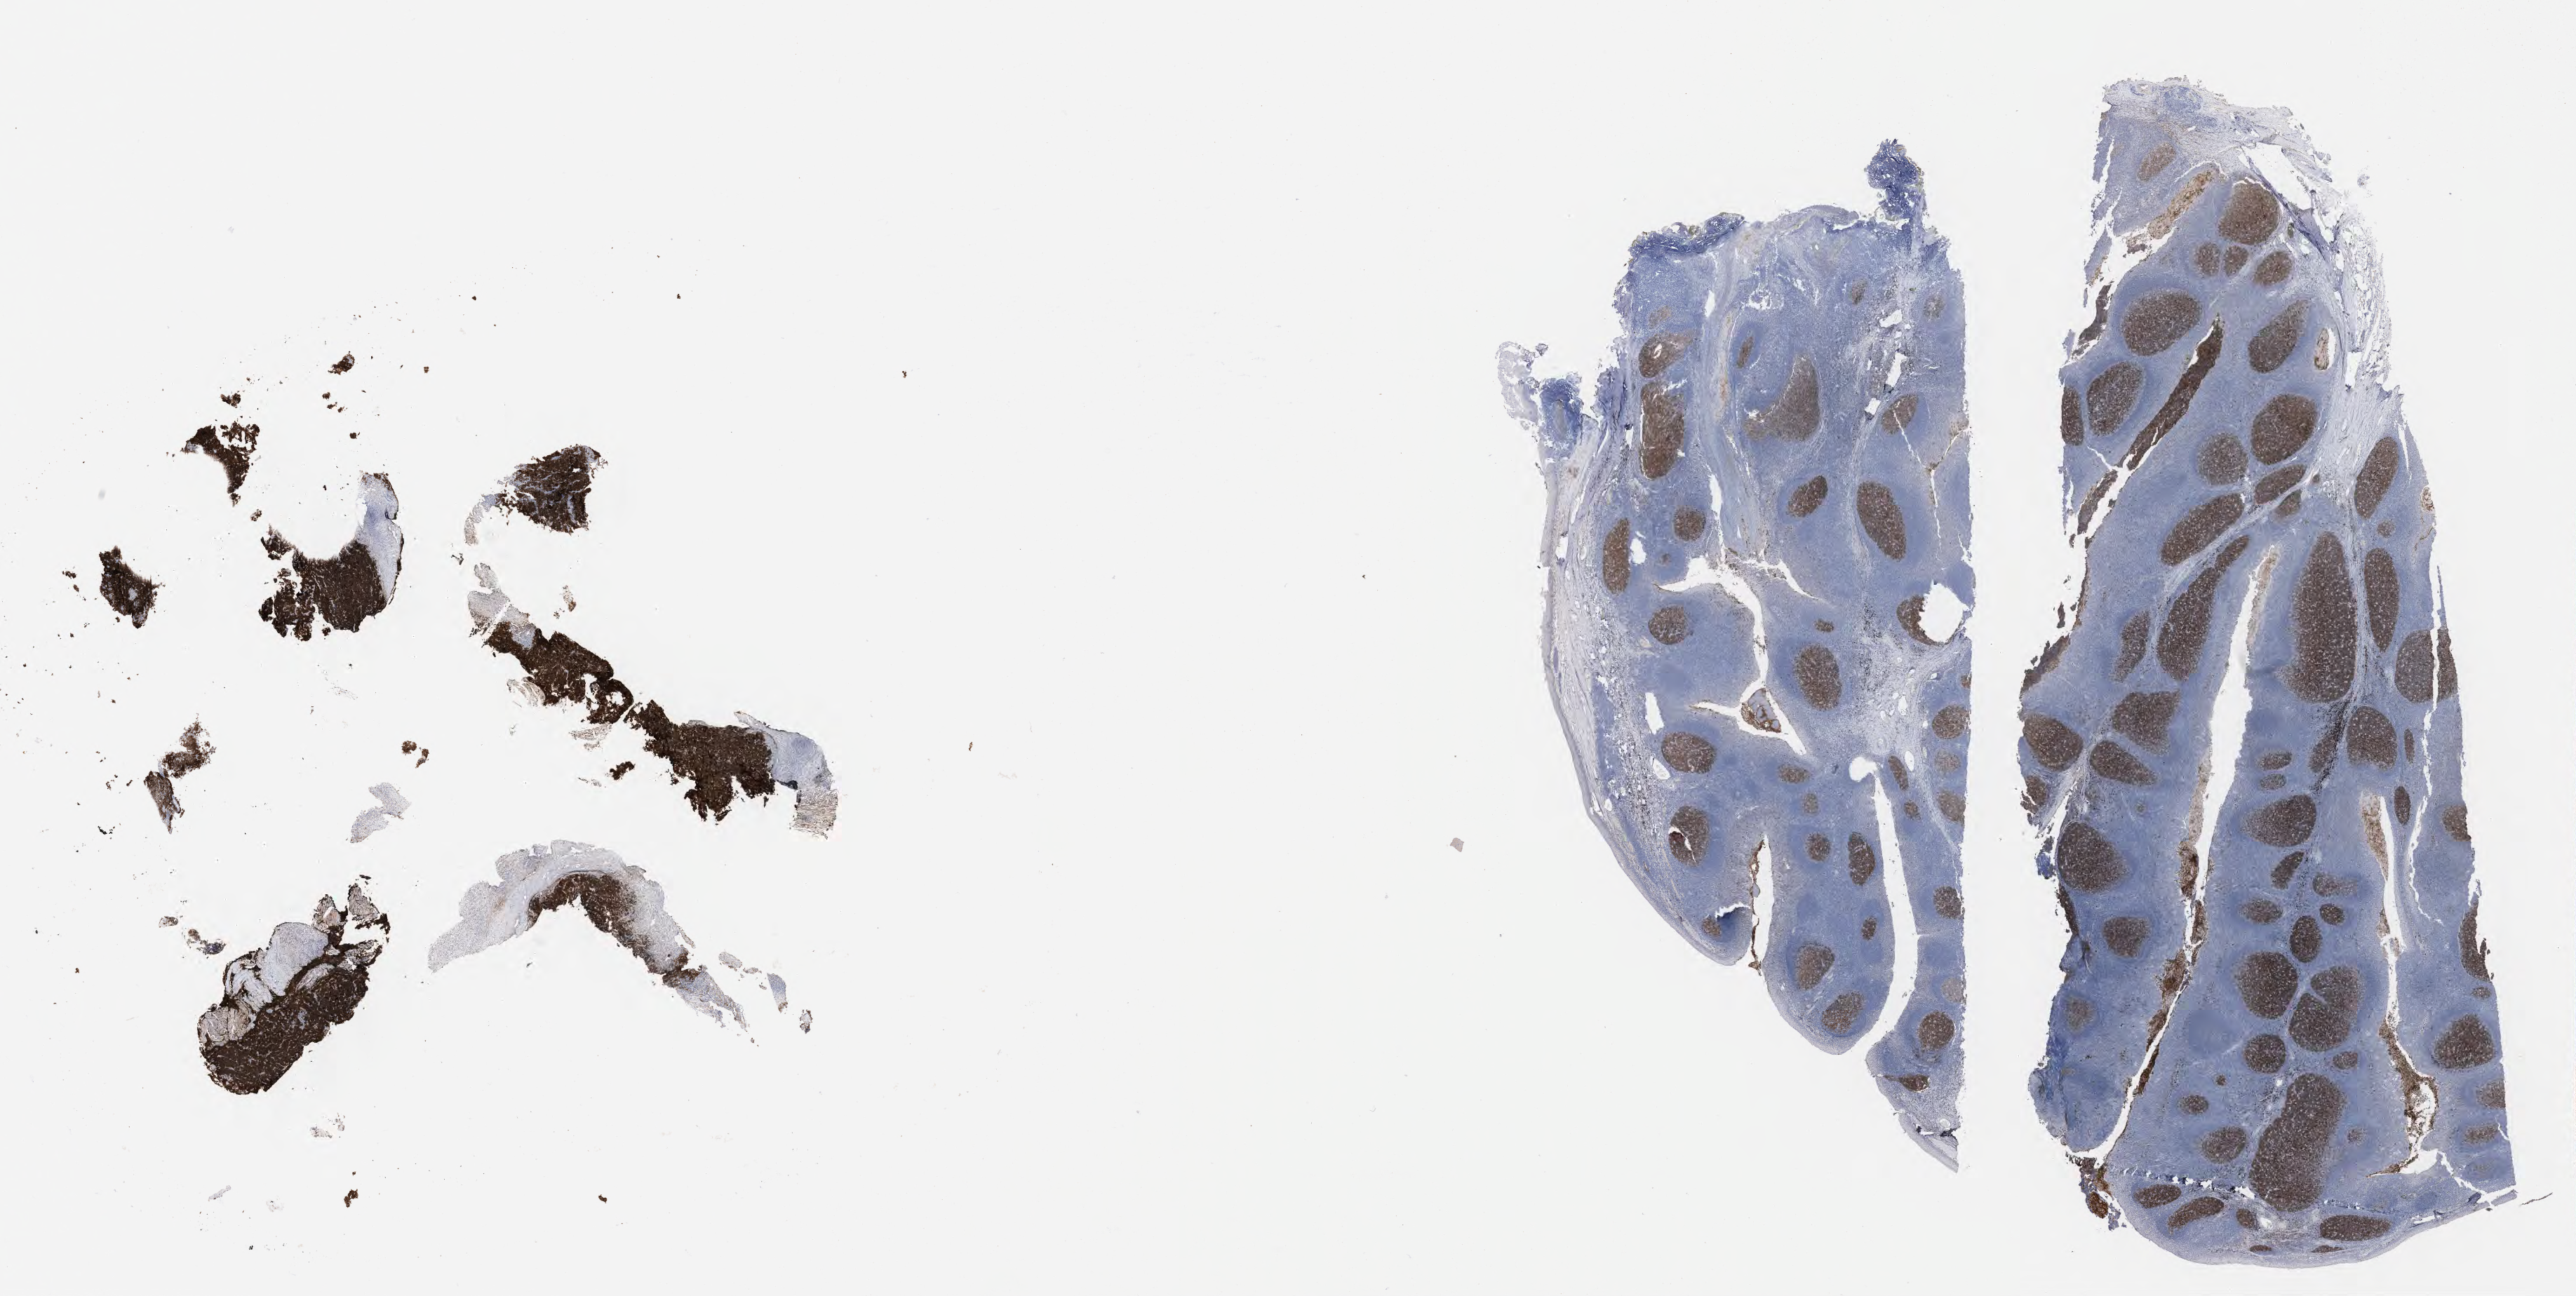
IHC for CD10, whole-slide image — low-resolution overview of the scanned area, about 29.7 x 14.9 mm, specimen: tumor tissue. Female patient; age at initial diagnosis 9 years.
Histologic diagnosis: Burkitt lymphoma, NOS.